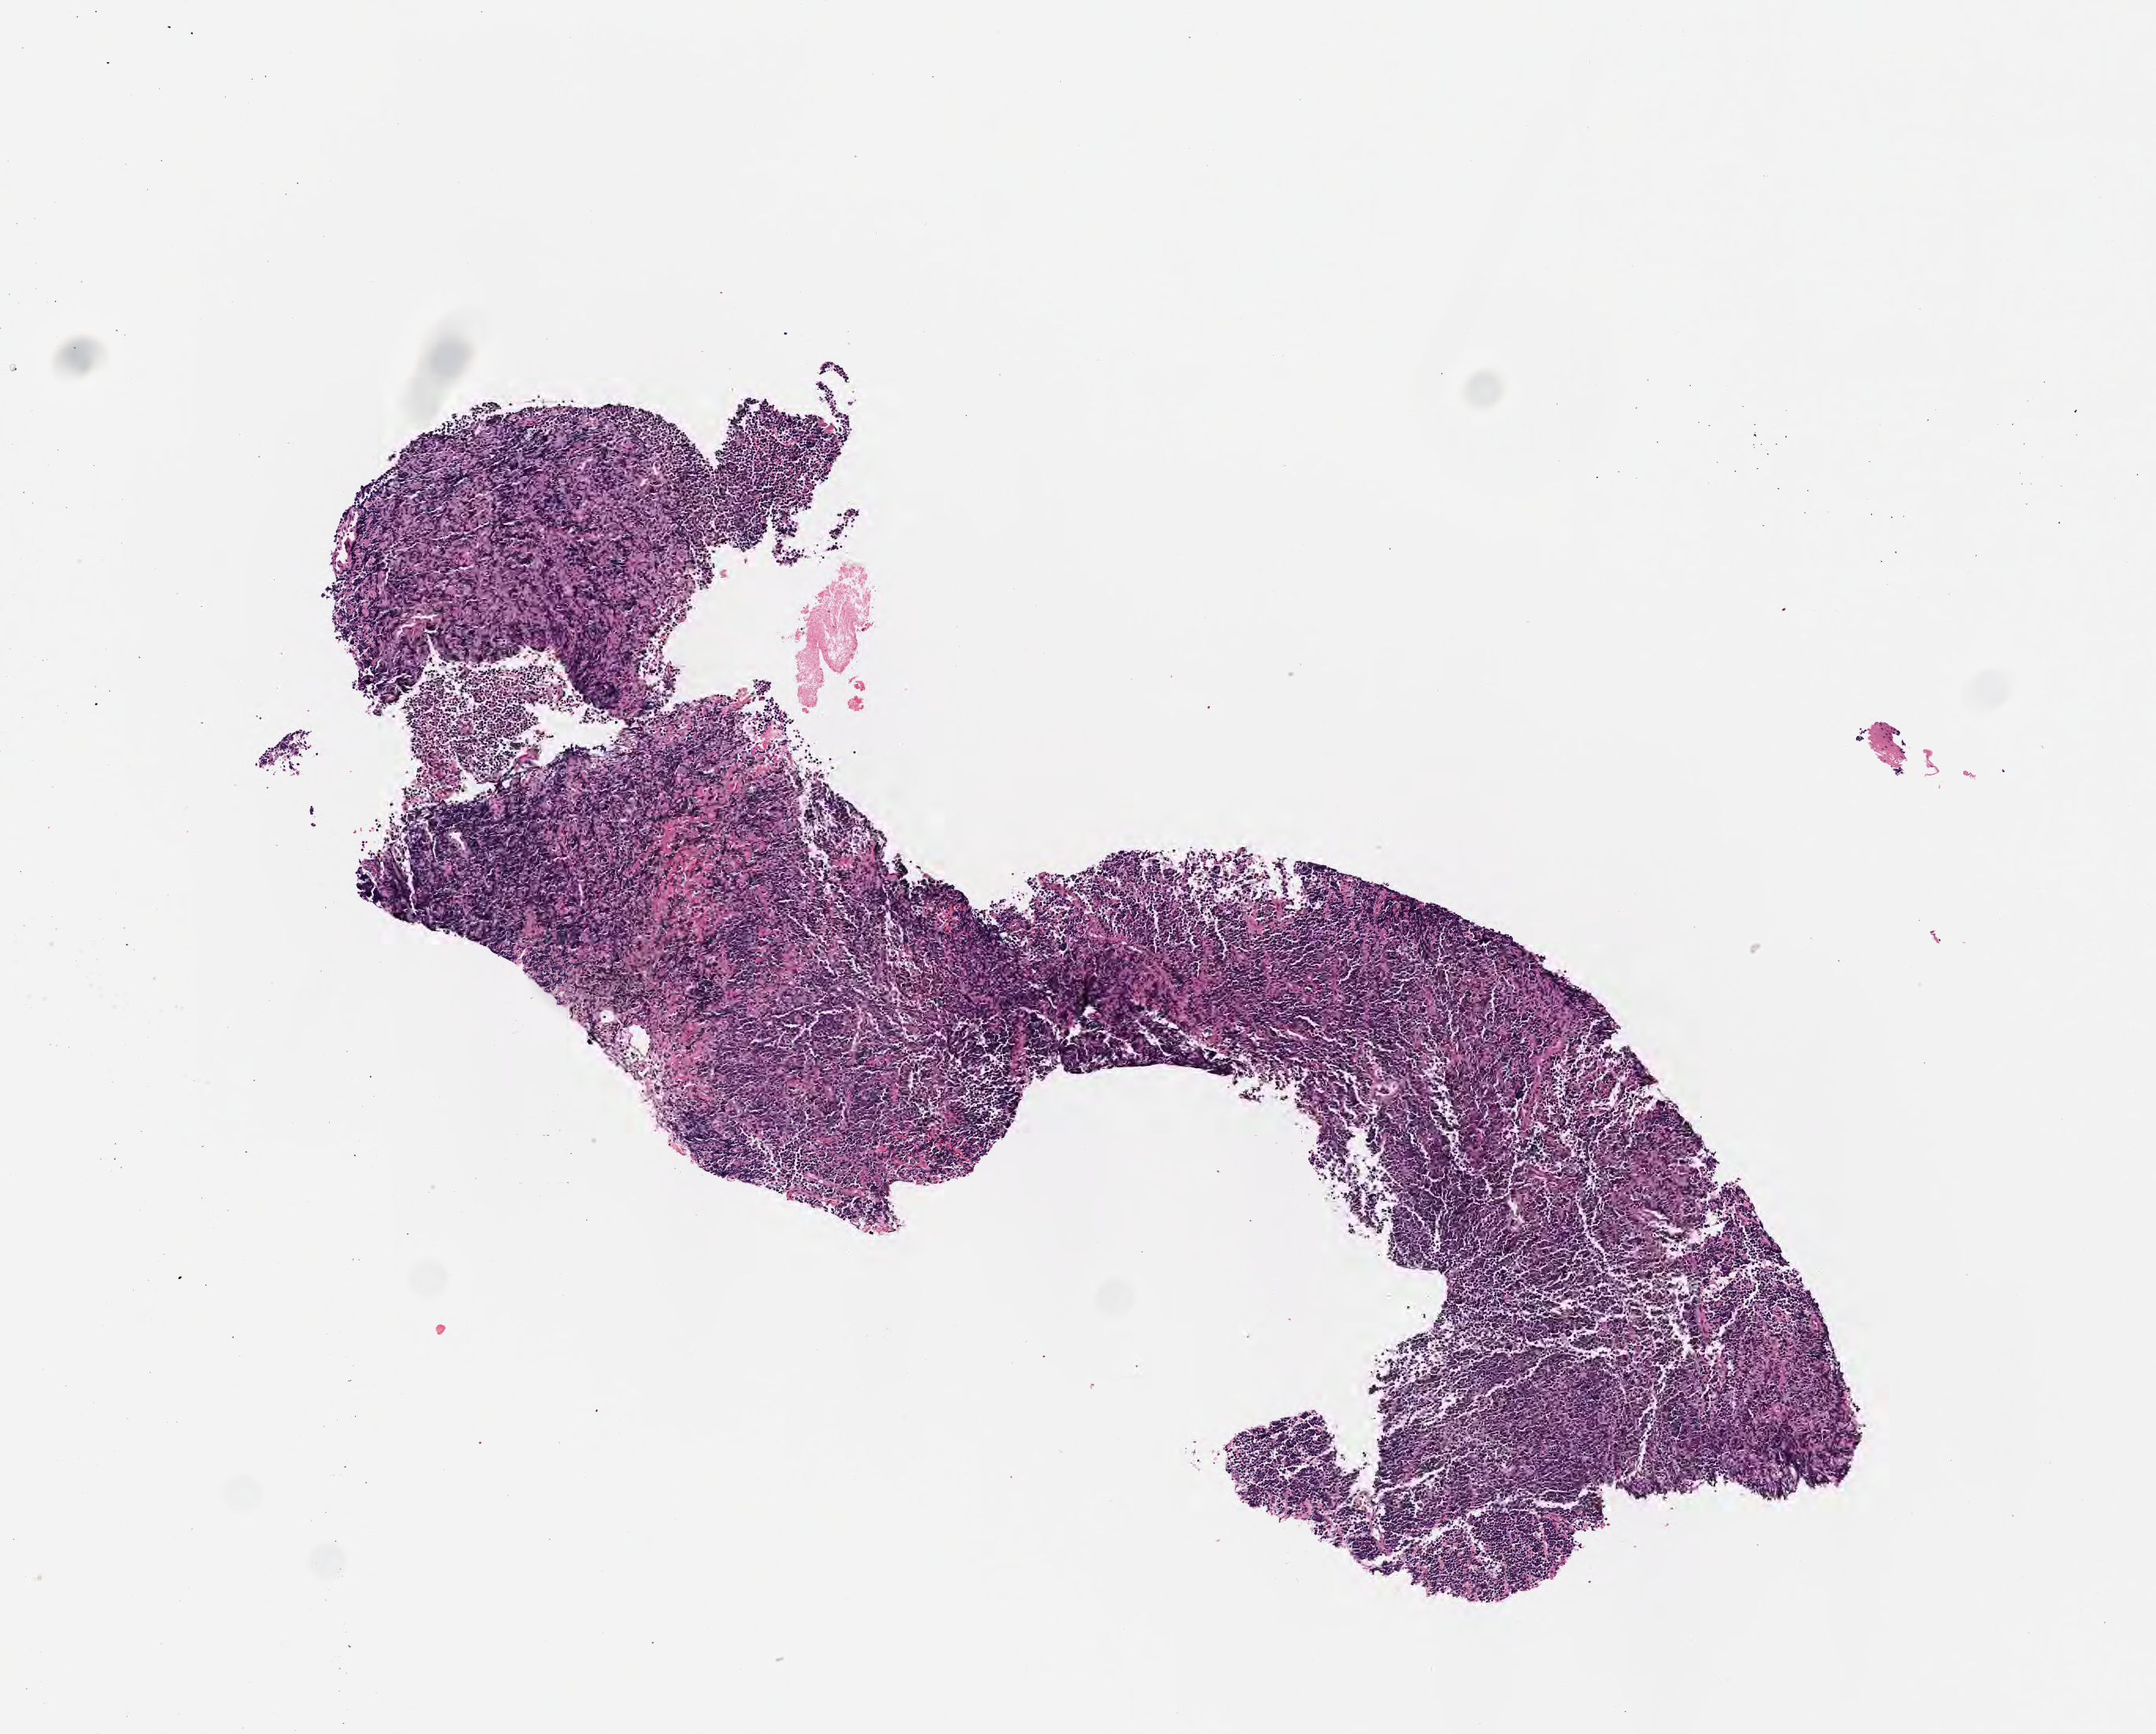
Whole-slide image, haematoxylin and eosin stain, whole scanned area (about 5.5 x 4.5 mm) shown as a low-resolution overview. Formalin-fixed, paraffin-embedded (FFPE) tissue. Specimen: primary tumor. Site: mandible. Female patient; age at initial diagnosis 5 years.
Diagnosis: Burkitt lymphoma, NOS.